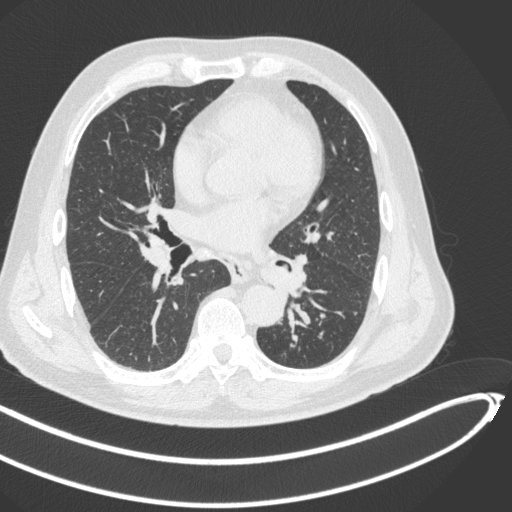
Chest CT, one axial slice; slice 237 of 466 in the series (ordered by position); 120 kVp; lung window (W 1500 / L -600 HU); 512 × 512 image matrix, field of view 400 × 400 mm. Male patient, age 64 years. From the clinical record (not read from this slice): clinical TNM (as recorded): T1c N0 M0.
Annotated regions visible in this slice (rectangle marked by the reading radiologist):
- lung tumour (recorded histology: squamous cell carcinoma): bounding box <252,257,302,303> (left, top, right, bottom; pixels)